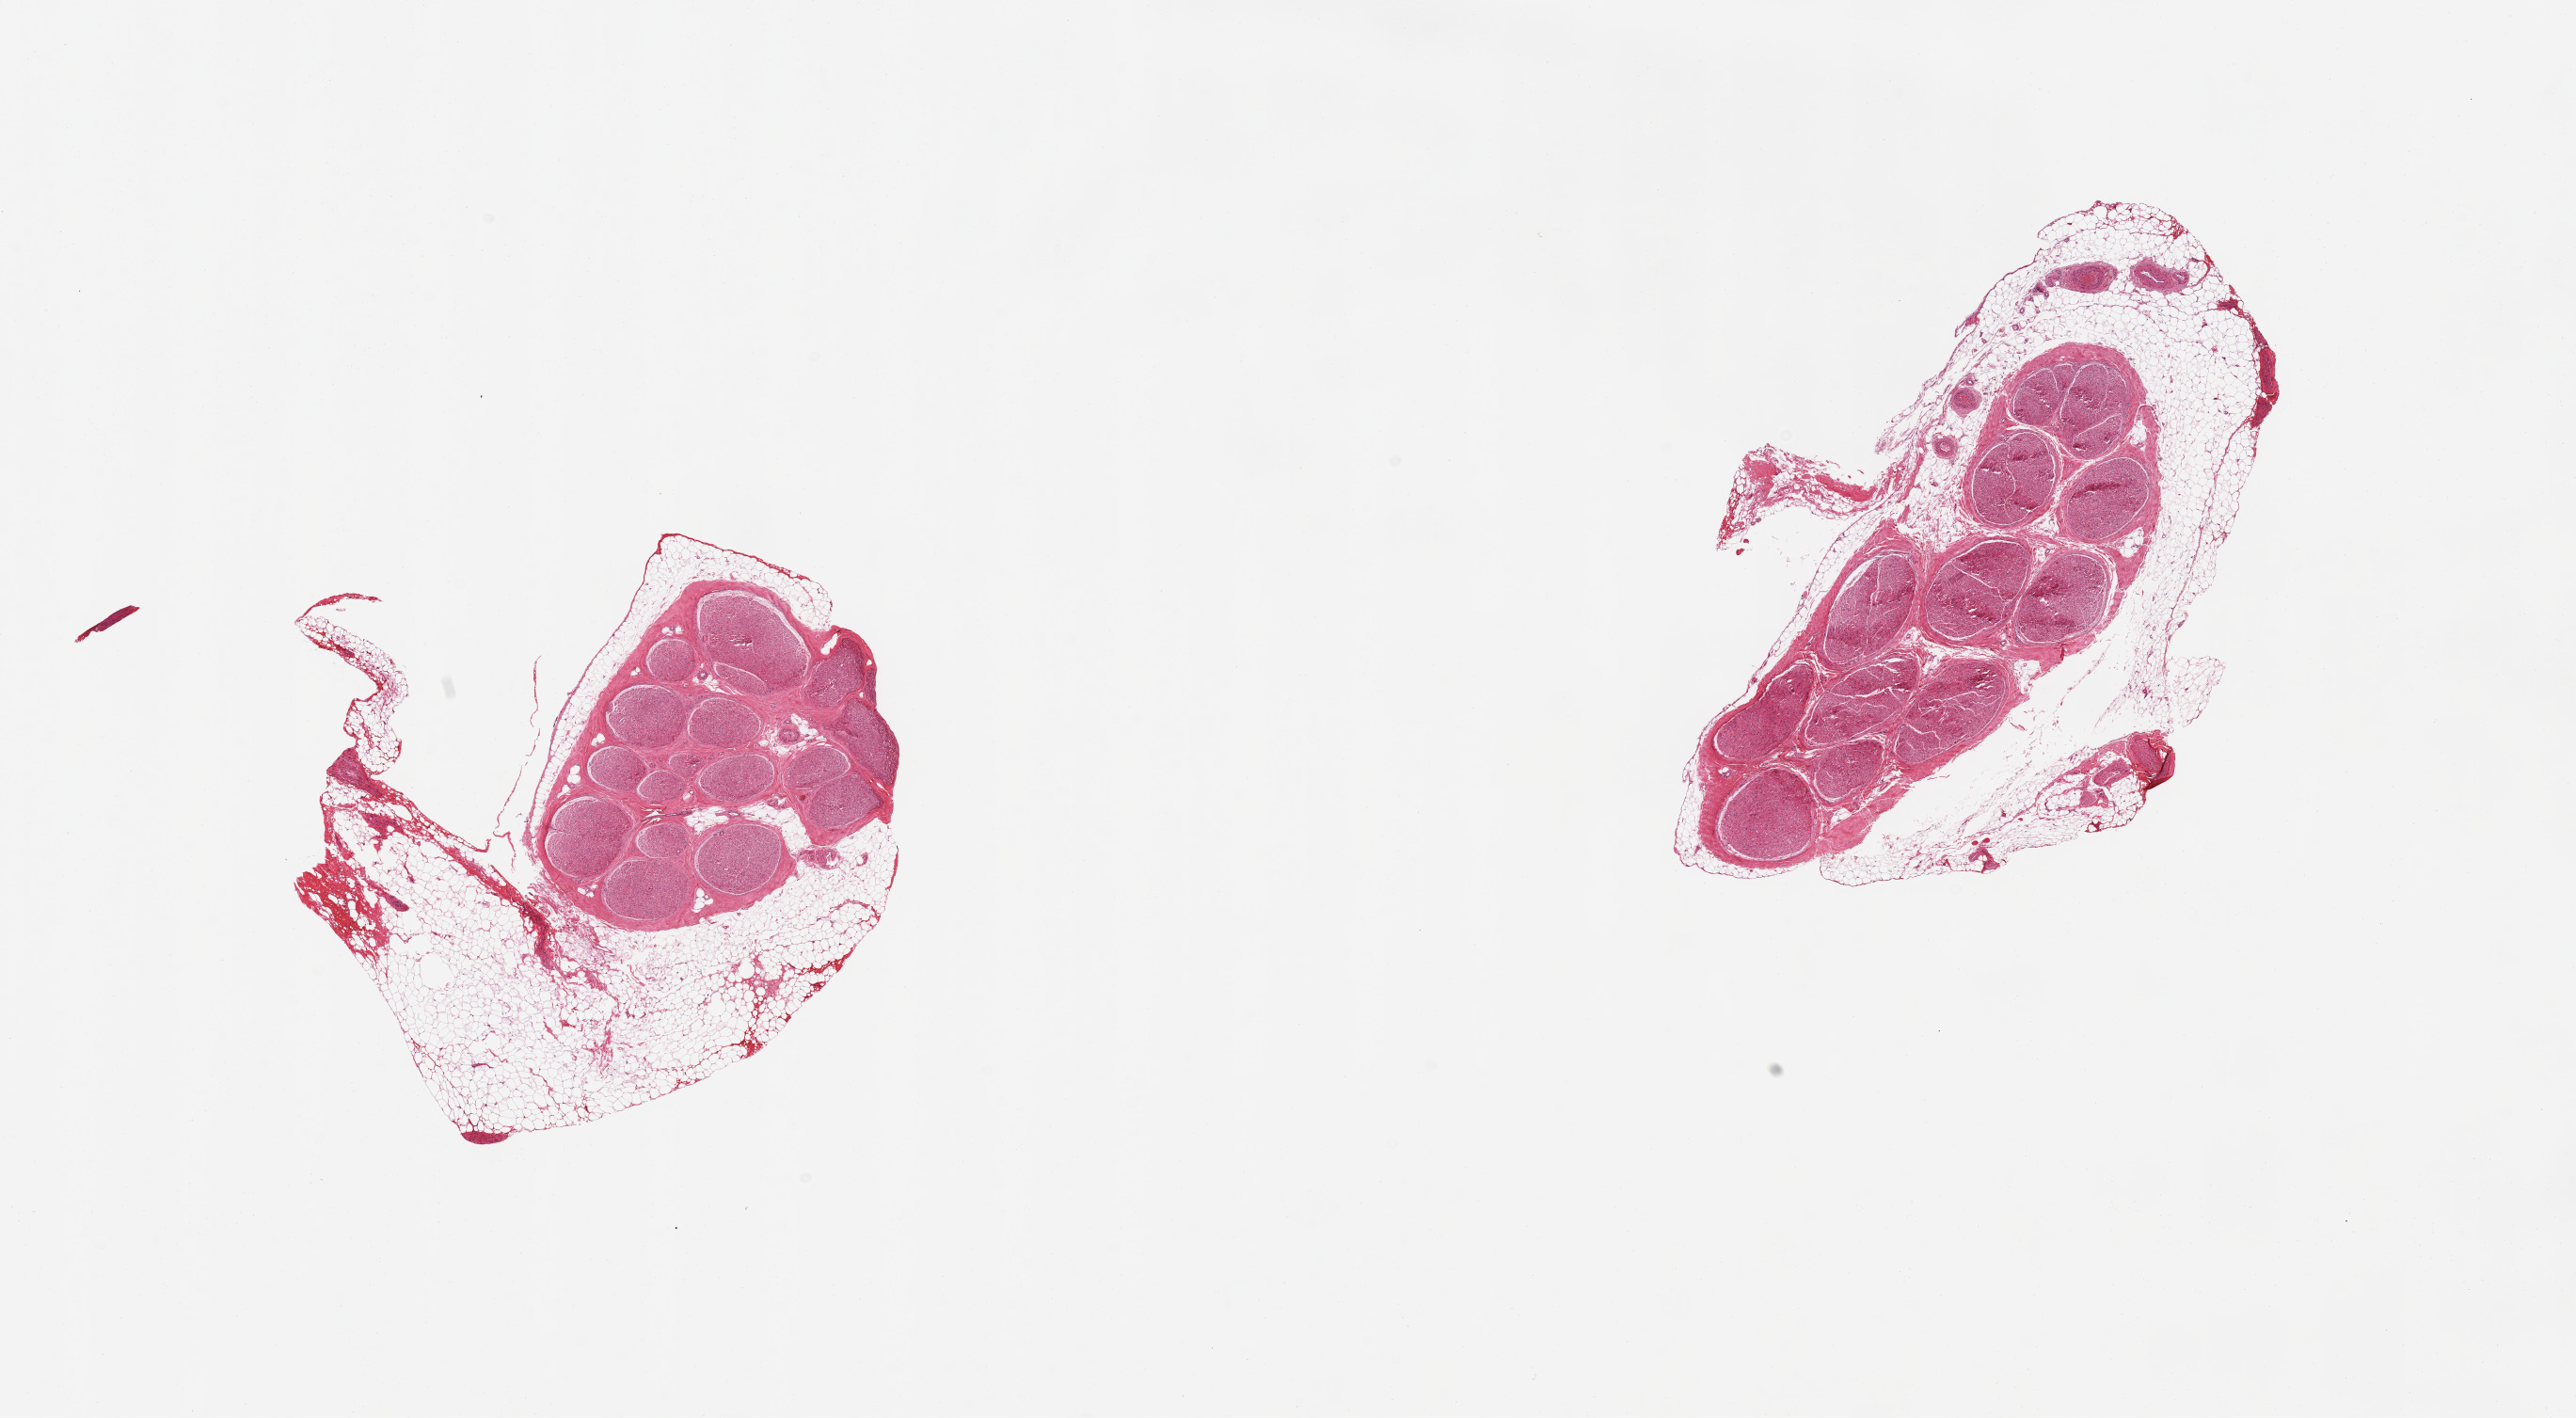
Hematoxylin and eosin (H&E) whole-slide image, brightfield — a low-resolution overview of the entire scanned area, about 21.7 x 11.9 mm; PAXgene-fixed, paraffin-embedded tissue; section of tibial nerve (target tissue); donor tissue sample. Donor: male.
Review note (as recorded): 2 pieces; 40% external fat.